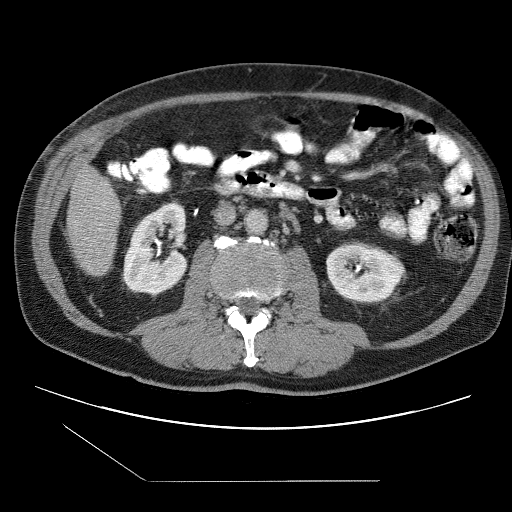
Contrast-enhanced abdominal CT (liver protocol), one axial slice; slice 19 of 109 in the series (ordered by position); reconstruction kernel STANDARD; 120 kVp; one of 2 acquisitions stored at this slice position; soft-tissue window (W 400 / L 40 HU); 512 × 512 image matrix, field of view 400 × 400 mm. From the clinical record (not read from this slice): diagnosis: hepatocellular carcinoma (patient treated with transarterial chemoembolisation; whether this scan precedes or follows treatment is not stated here); TNM stage (as recorded): Stage-IIIB; Child-Pugh class: A; tumour differentiation: well differentiated; tumour nodularity: multinodular.
Structures marked on this image (semi-automatically segmented with operator editing):
- liver parenchyma outside the tumour (the mass and vessels are separate outlines, so this box may not span the whole liver): box from (x=66, y=166) to (x=120, y=274) px